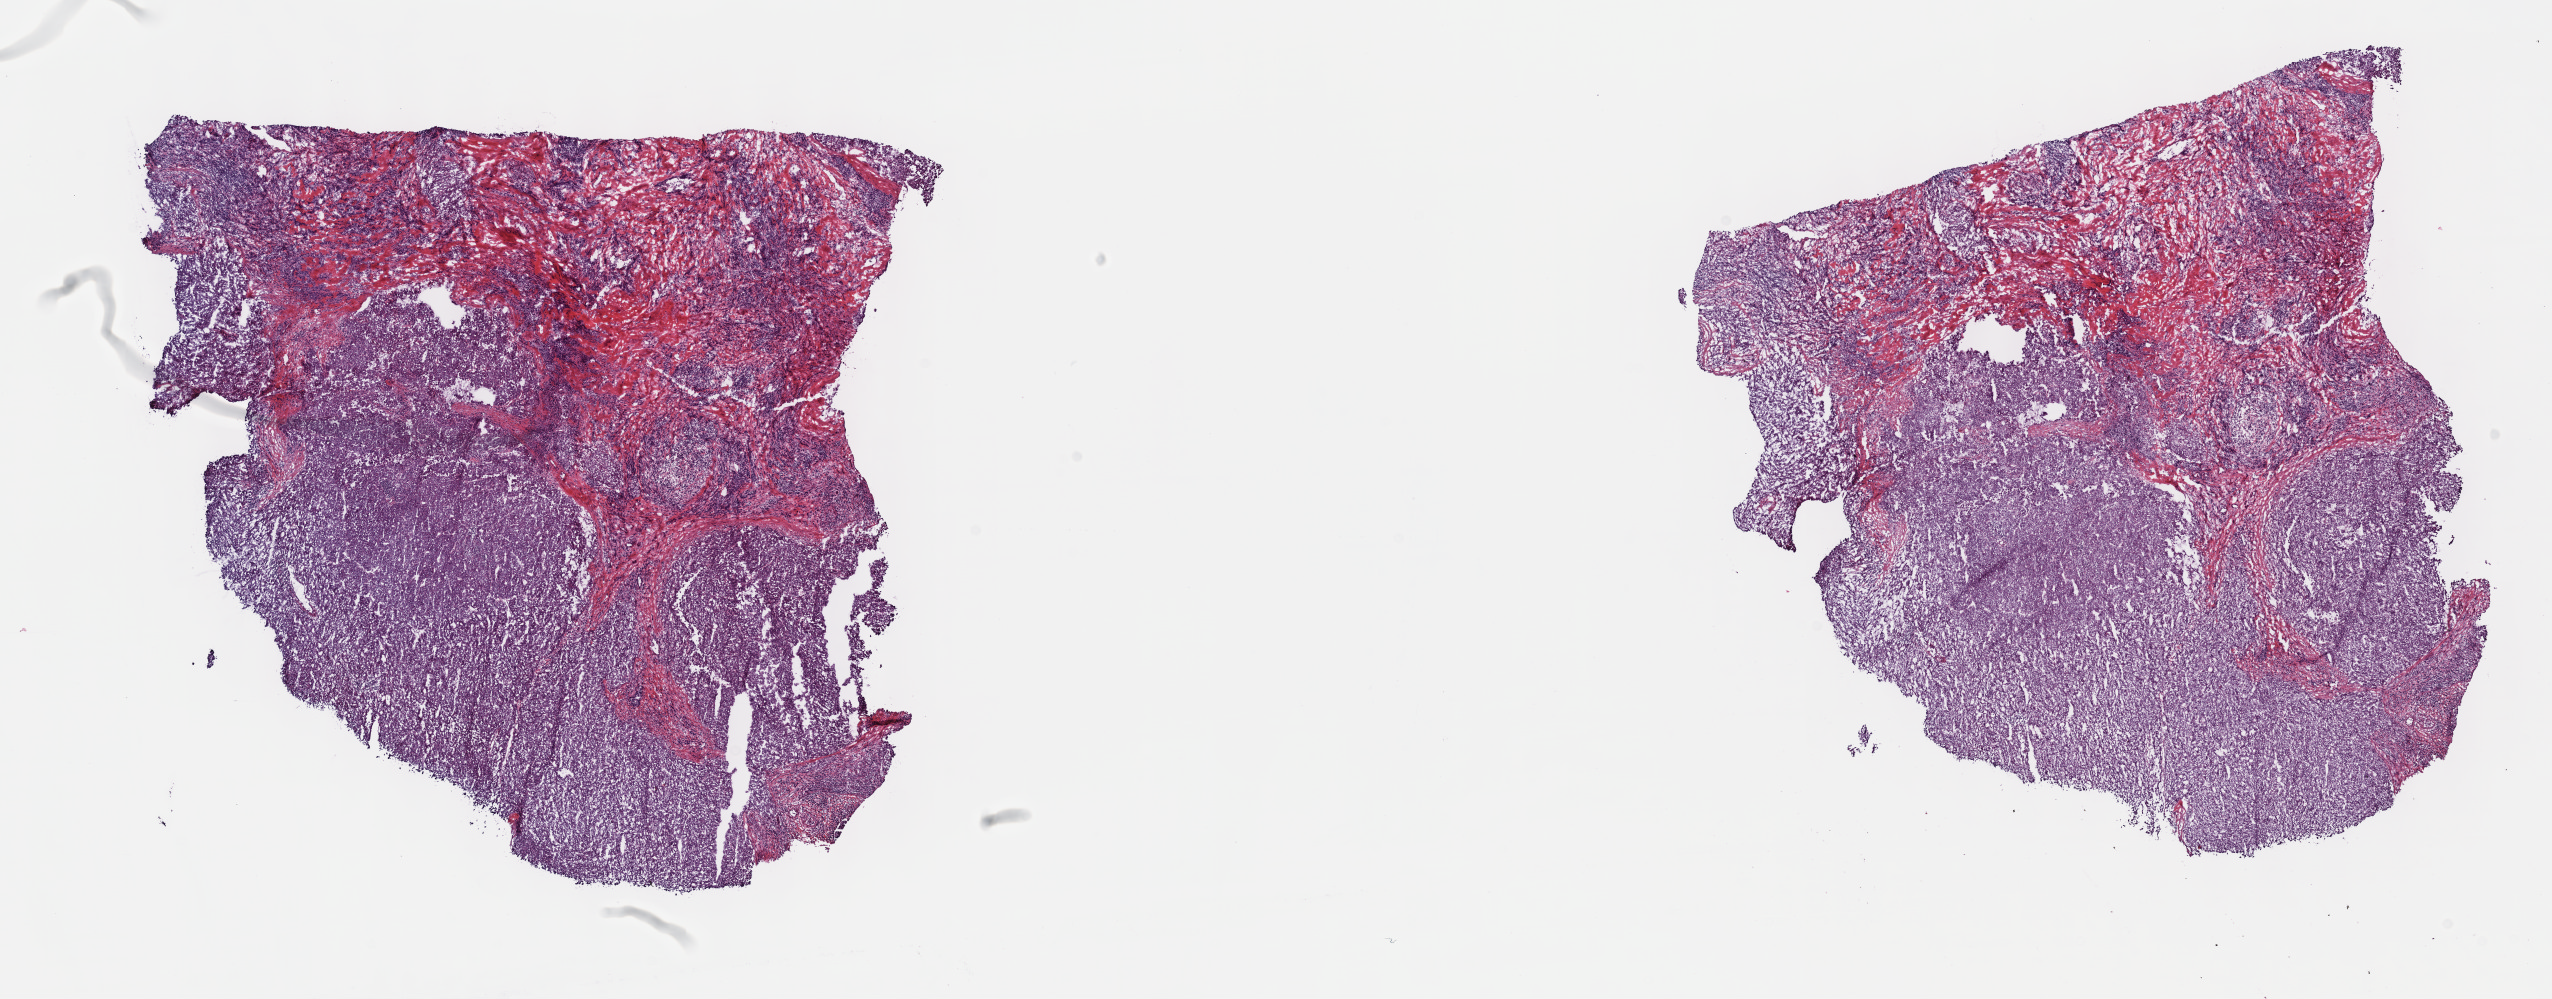
Digitized Hematoxylin and eosin (H&E) stained tissue section (whole slide) — a low-resolution overview of the entire scanned area, about 20.6 x 8.1 mm (slide scanned at 40x); frozen section from the top of the tissue portion; primary tumour sample from the liver. Male, age 61 years at initial diagnosis. Histologic grade: G1 (well differentiated). Pathologist review of this section (percent, as recorded): tumour cells 53%, tumour nuclei 68%, normal cells 0%, stromal cells 35%, necrosis 12%. Infiltration values recorded for this section: lymphocyte infiltration 24%, monocyte infiltration 2%, neutrophil infiltration 4%.
• AJCC pathologic stage: II
• diagnosis: Combined hepatocellular carcinoma and cholangiocarcinoma